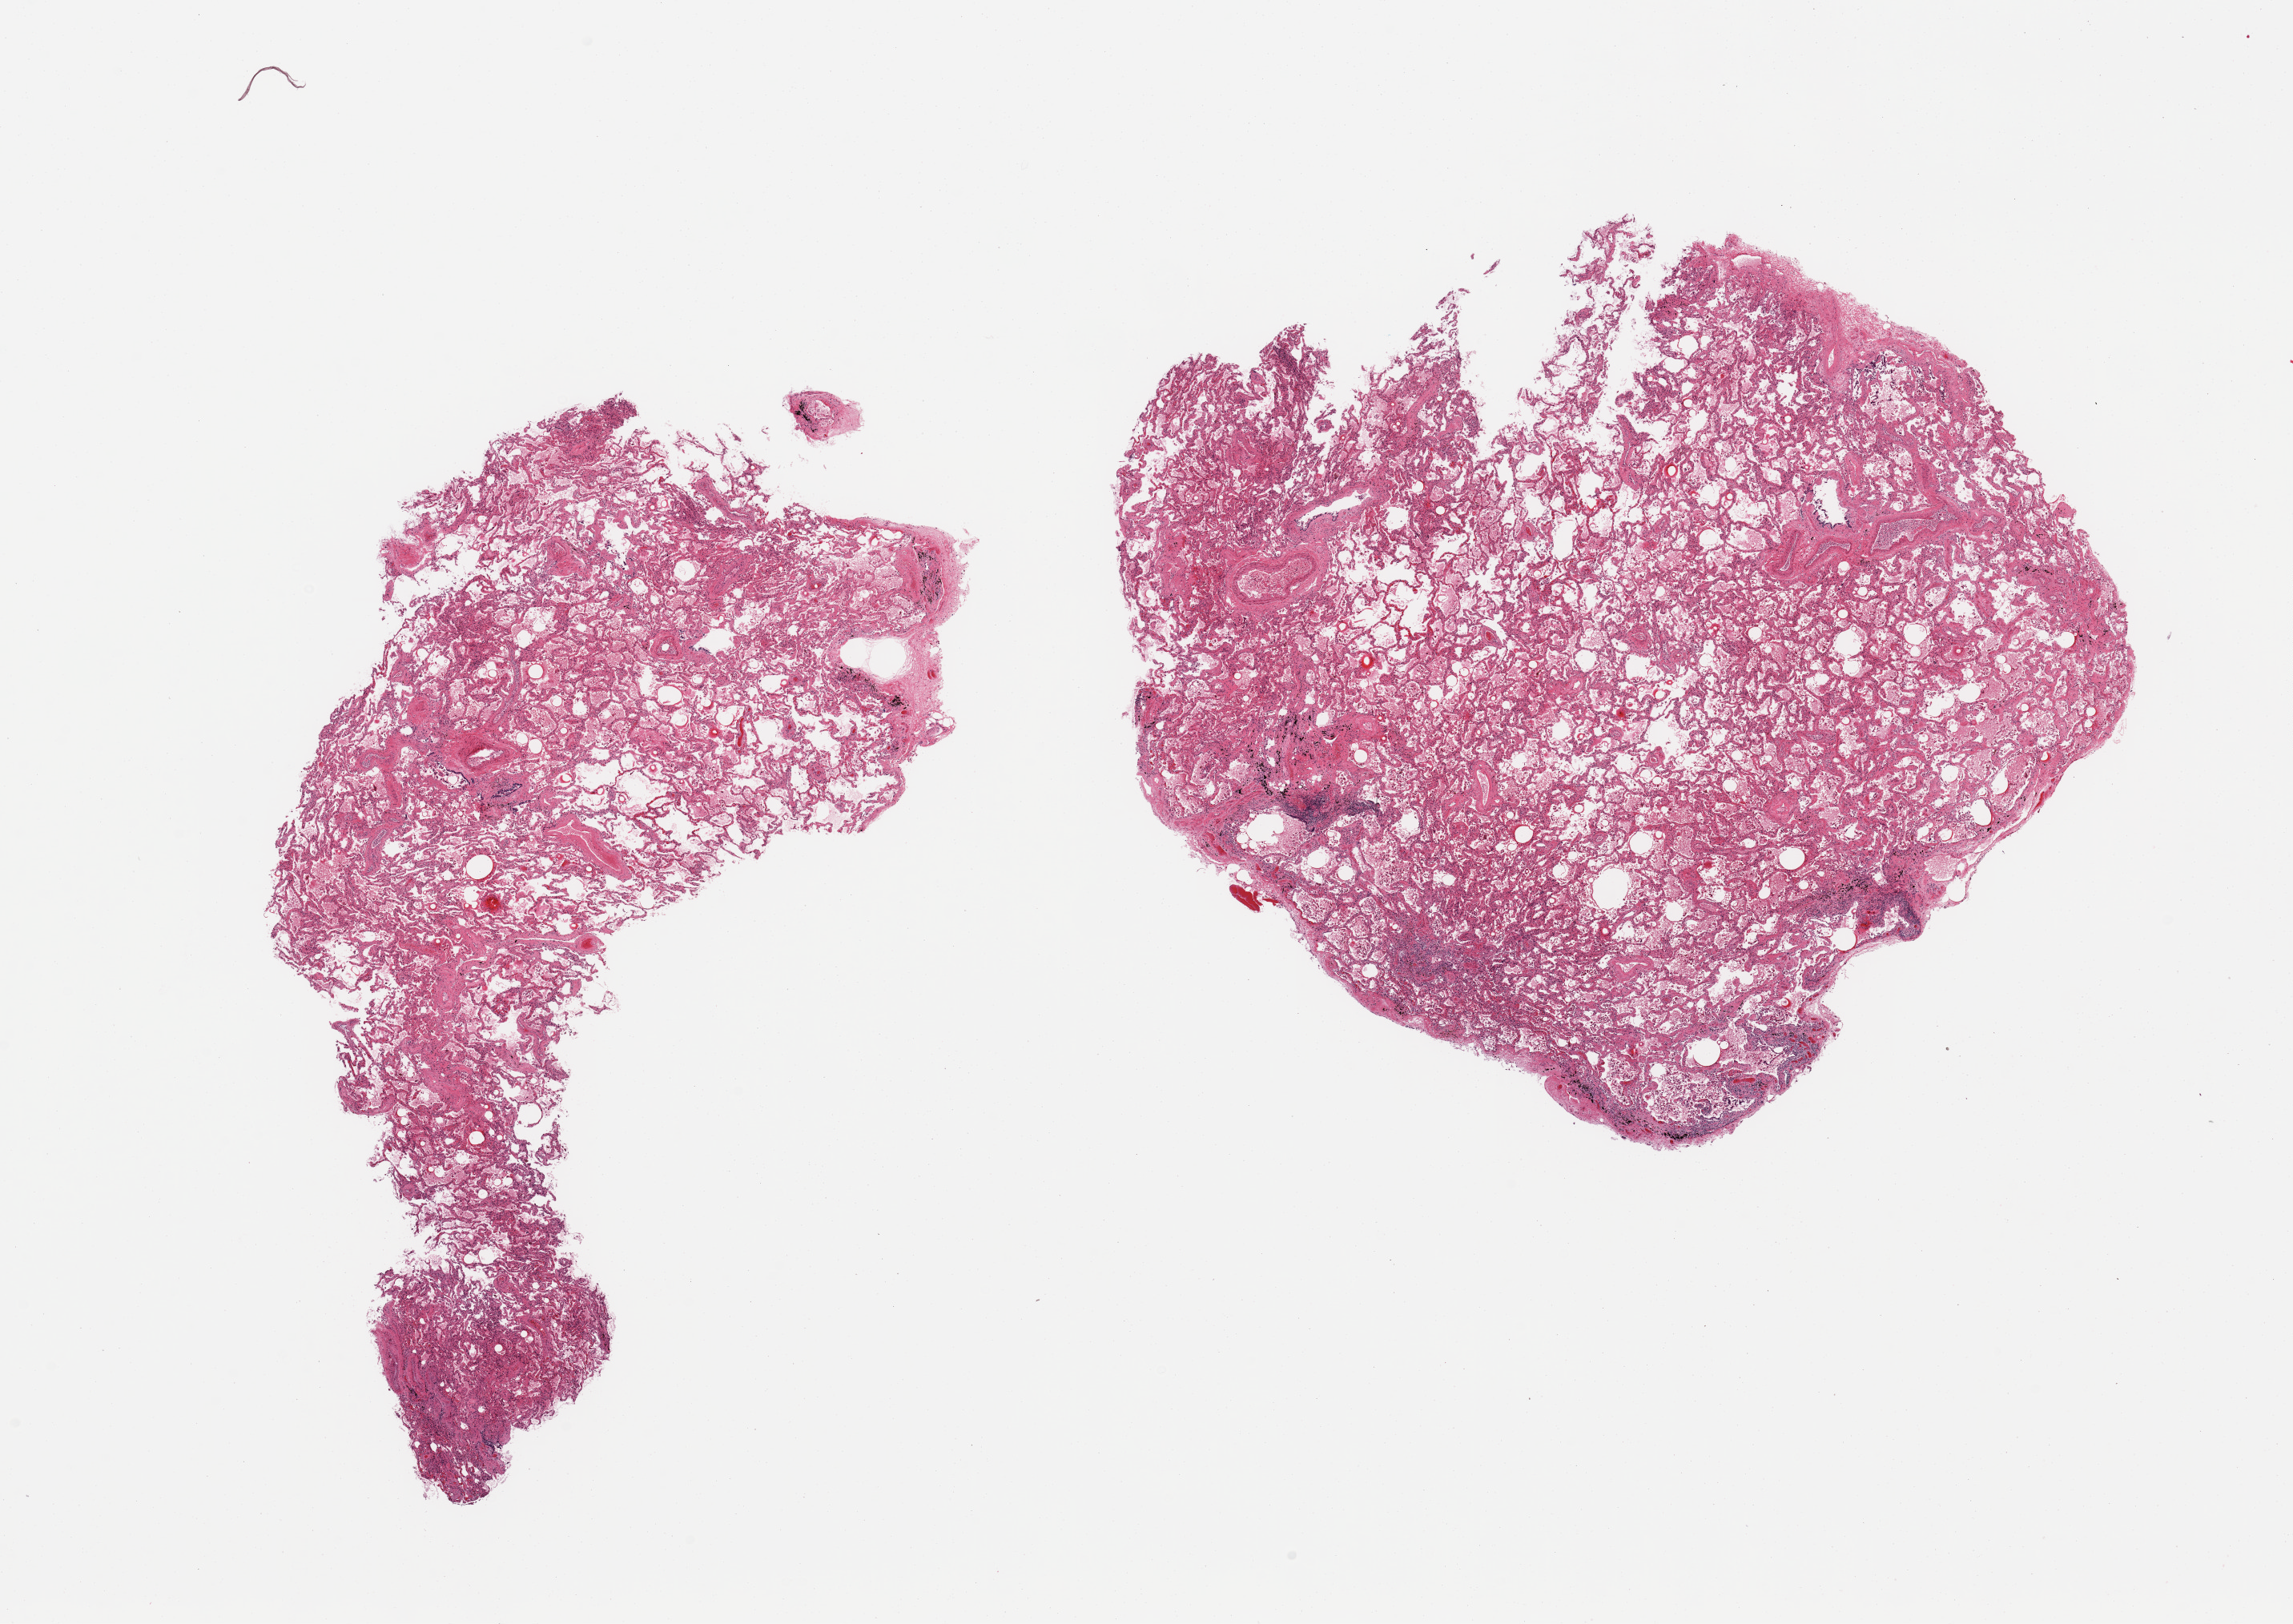
Hematoxylin and eosin (H&E) whole-slide image — shown as a low-resolution overview of the whole scanned area (about 22.6 x 16.0 mm, acquisition: 20x scan), PAXgene-fixed, paraffin-embedded tissue, section of lung (target tissue), donor tissue sample. Donor: male.
- reviewer comment on this tissue sample: 2 pieces, moderate congestion